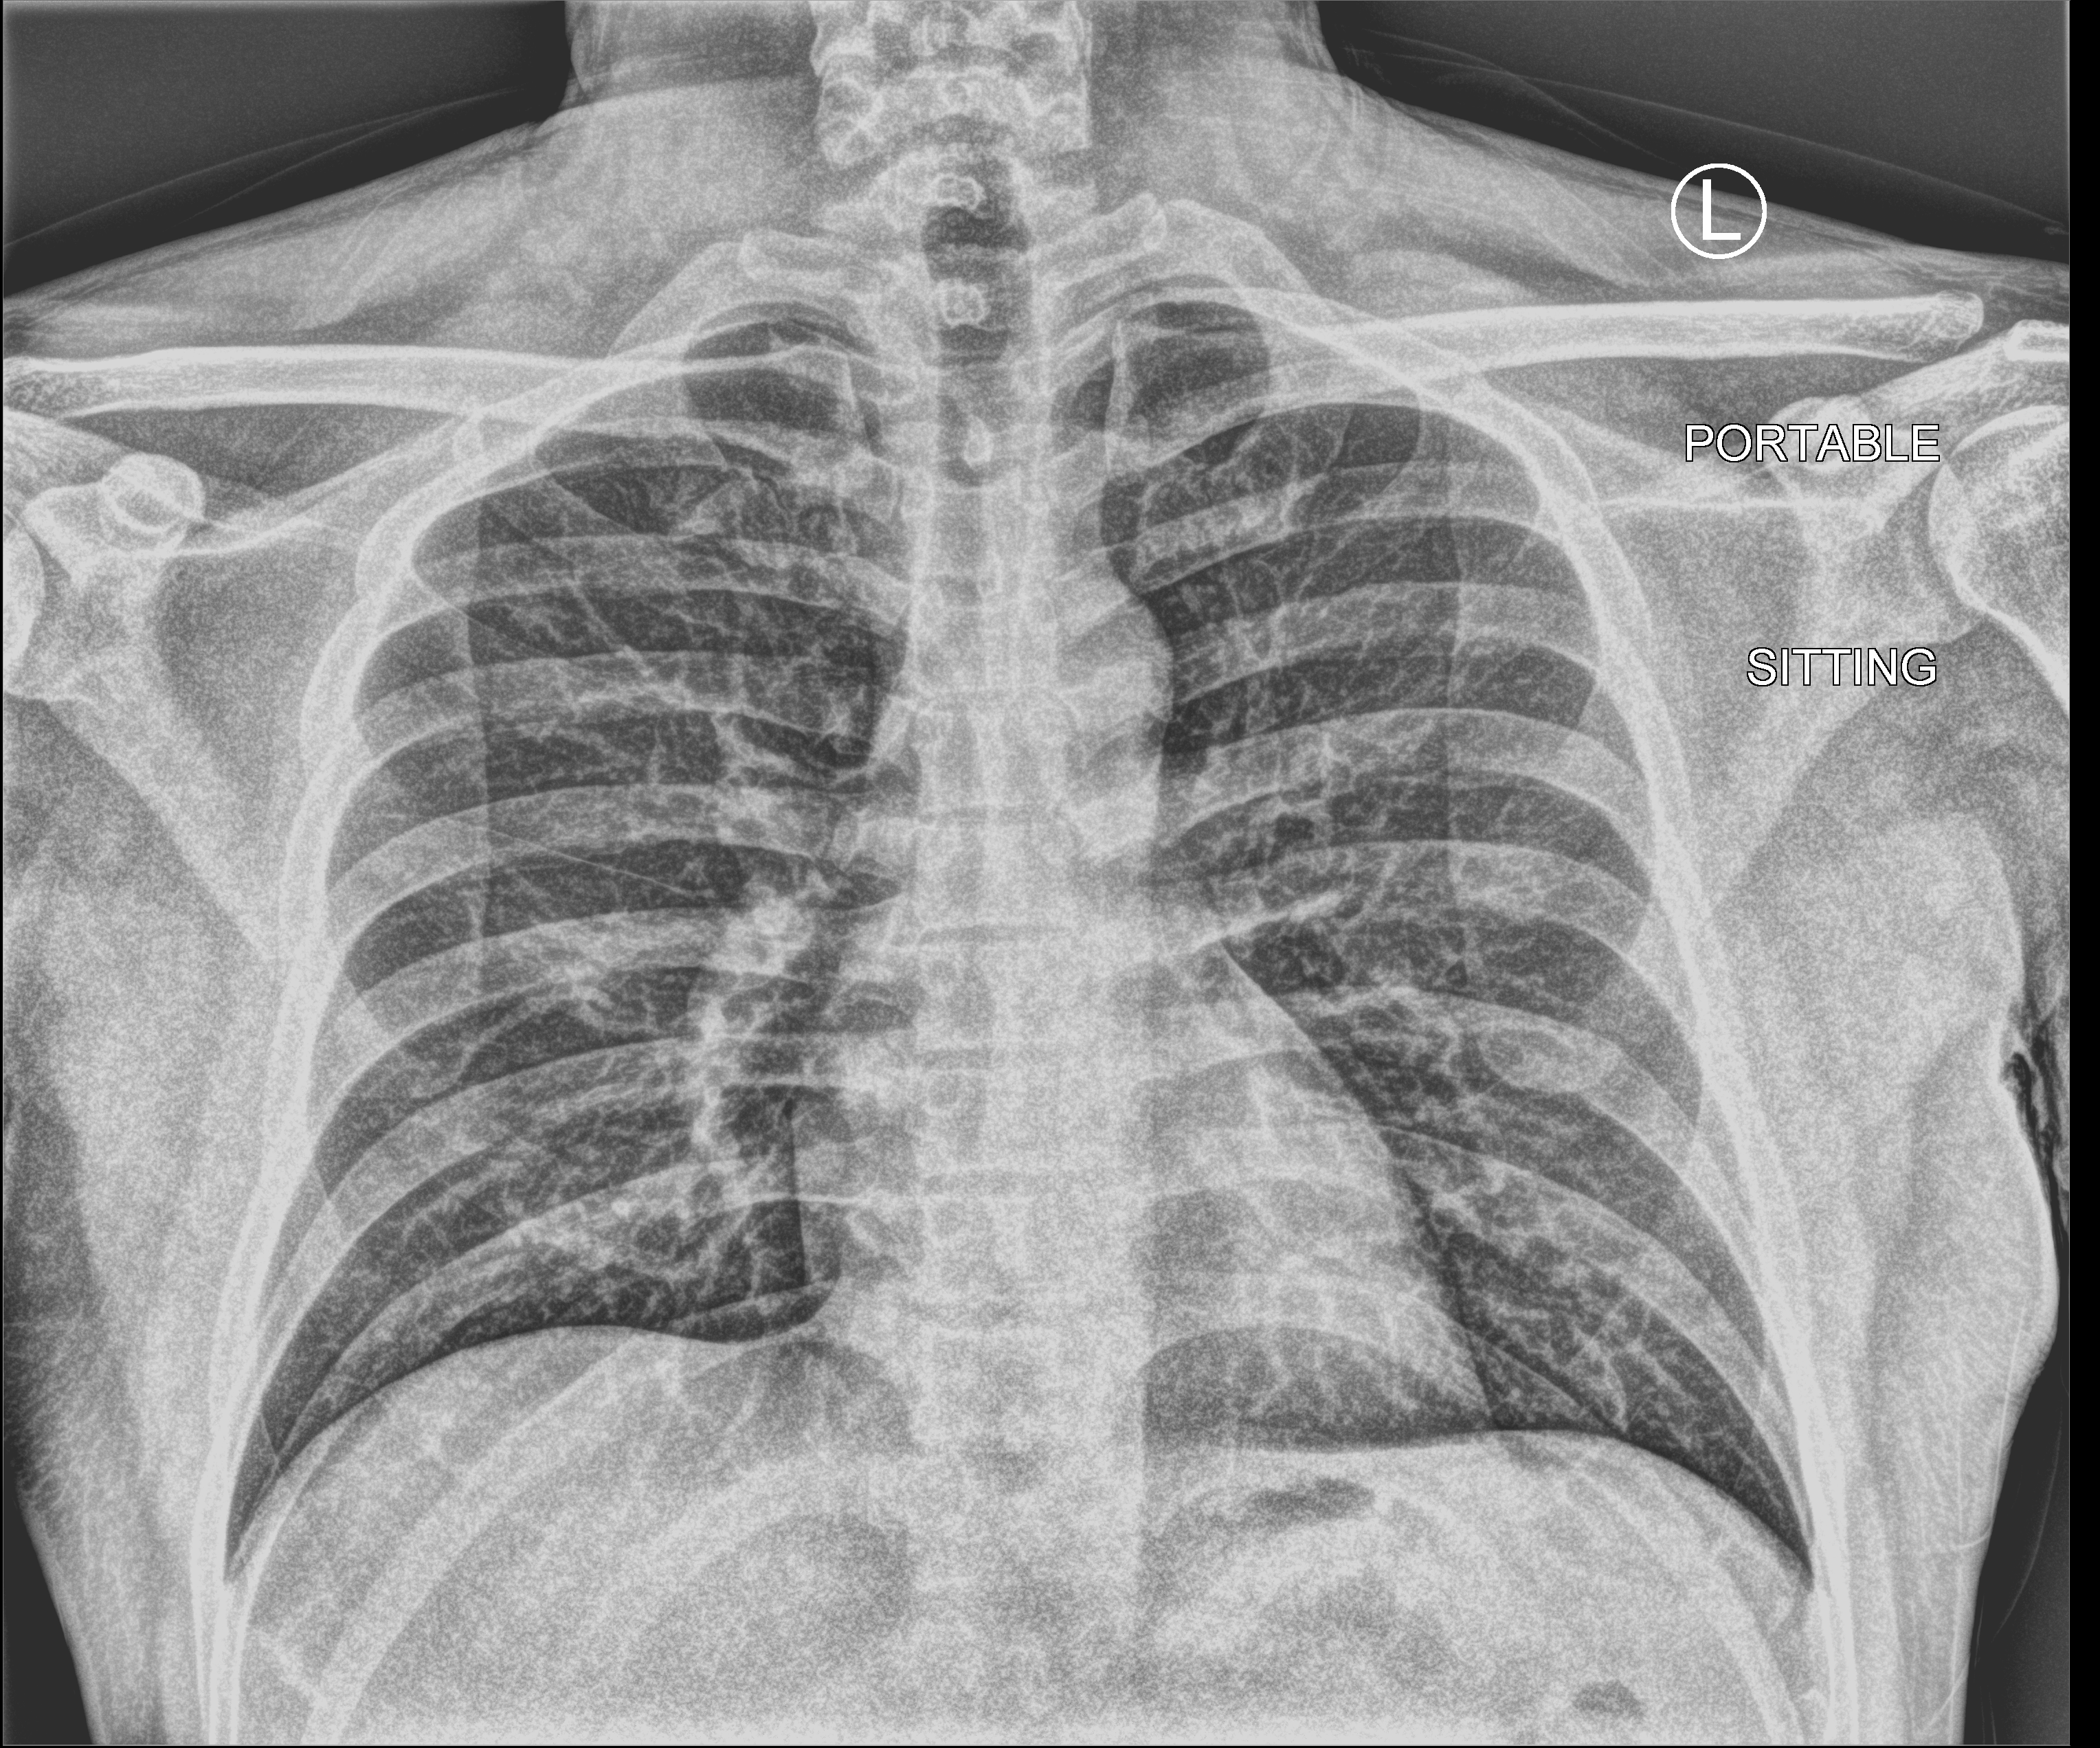
Chest X-ray (portable), anteroposterior (AP) projection. Patient hospitalised with COVID-19; male, aged 18–59 years.
Hospital-stay facts (about this admission, not read from this image; timing relative to this image not recorded):
- admitted to intensive care during this hospital stay: no